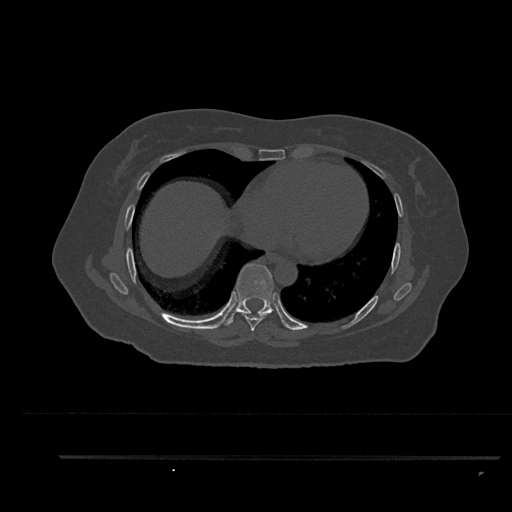
CT including the spine, one axial slice; position 483 of 797 along the scan axis; reconstruction kernel Br40s/3; bone window (W 1800 / L 400 HU); 512 × 512 image matrix, field of view 408 × 408 mm. Female patient, age 44 years. From the clinical record (not read from this slice): primary cancer: renal; vertebrae with lytic lesions (as recorded): L1.
Structures marked on this image (semi-automatic segmentation, software-assisted and operator-edited):
- T7 vertebra: bounding box (x1, y1, x2, y2) in pixels: (240, 312, 267, 333)
- T8 vertebra: (223, 264, 286, 327)